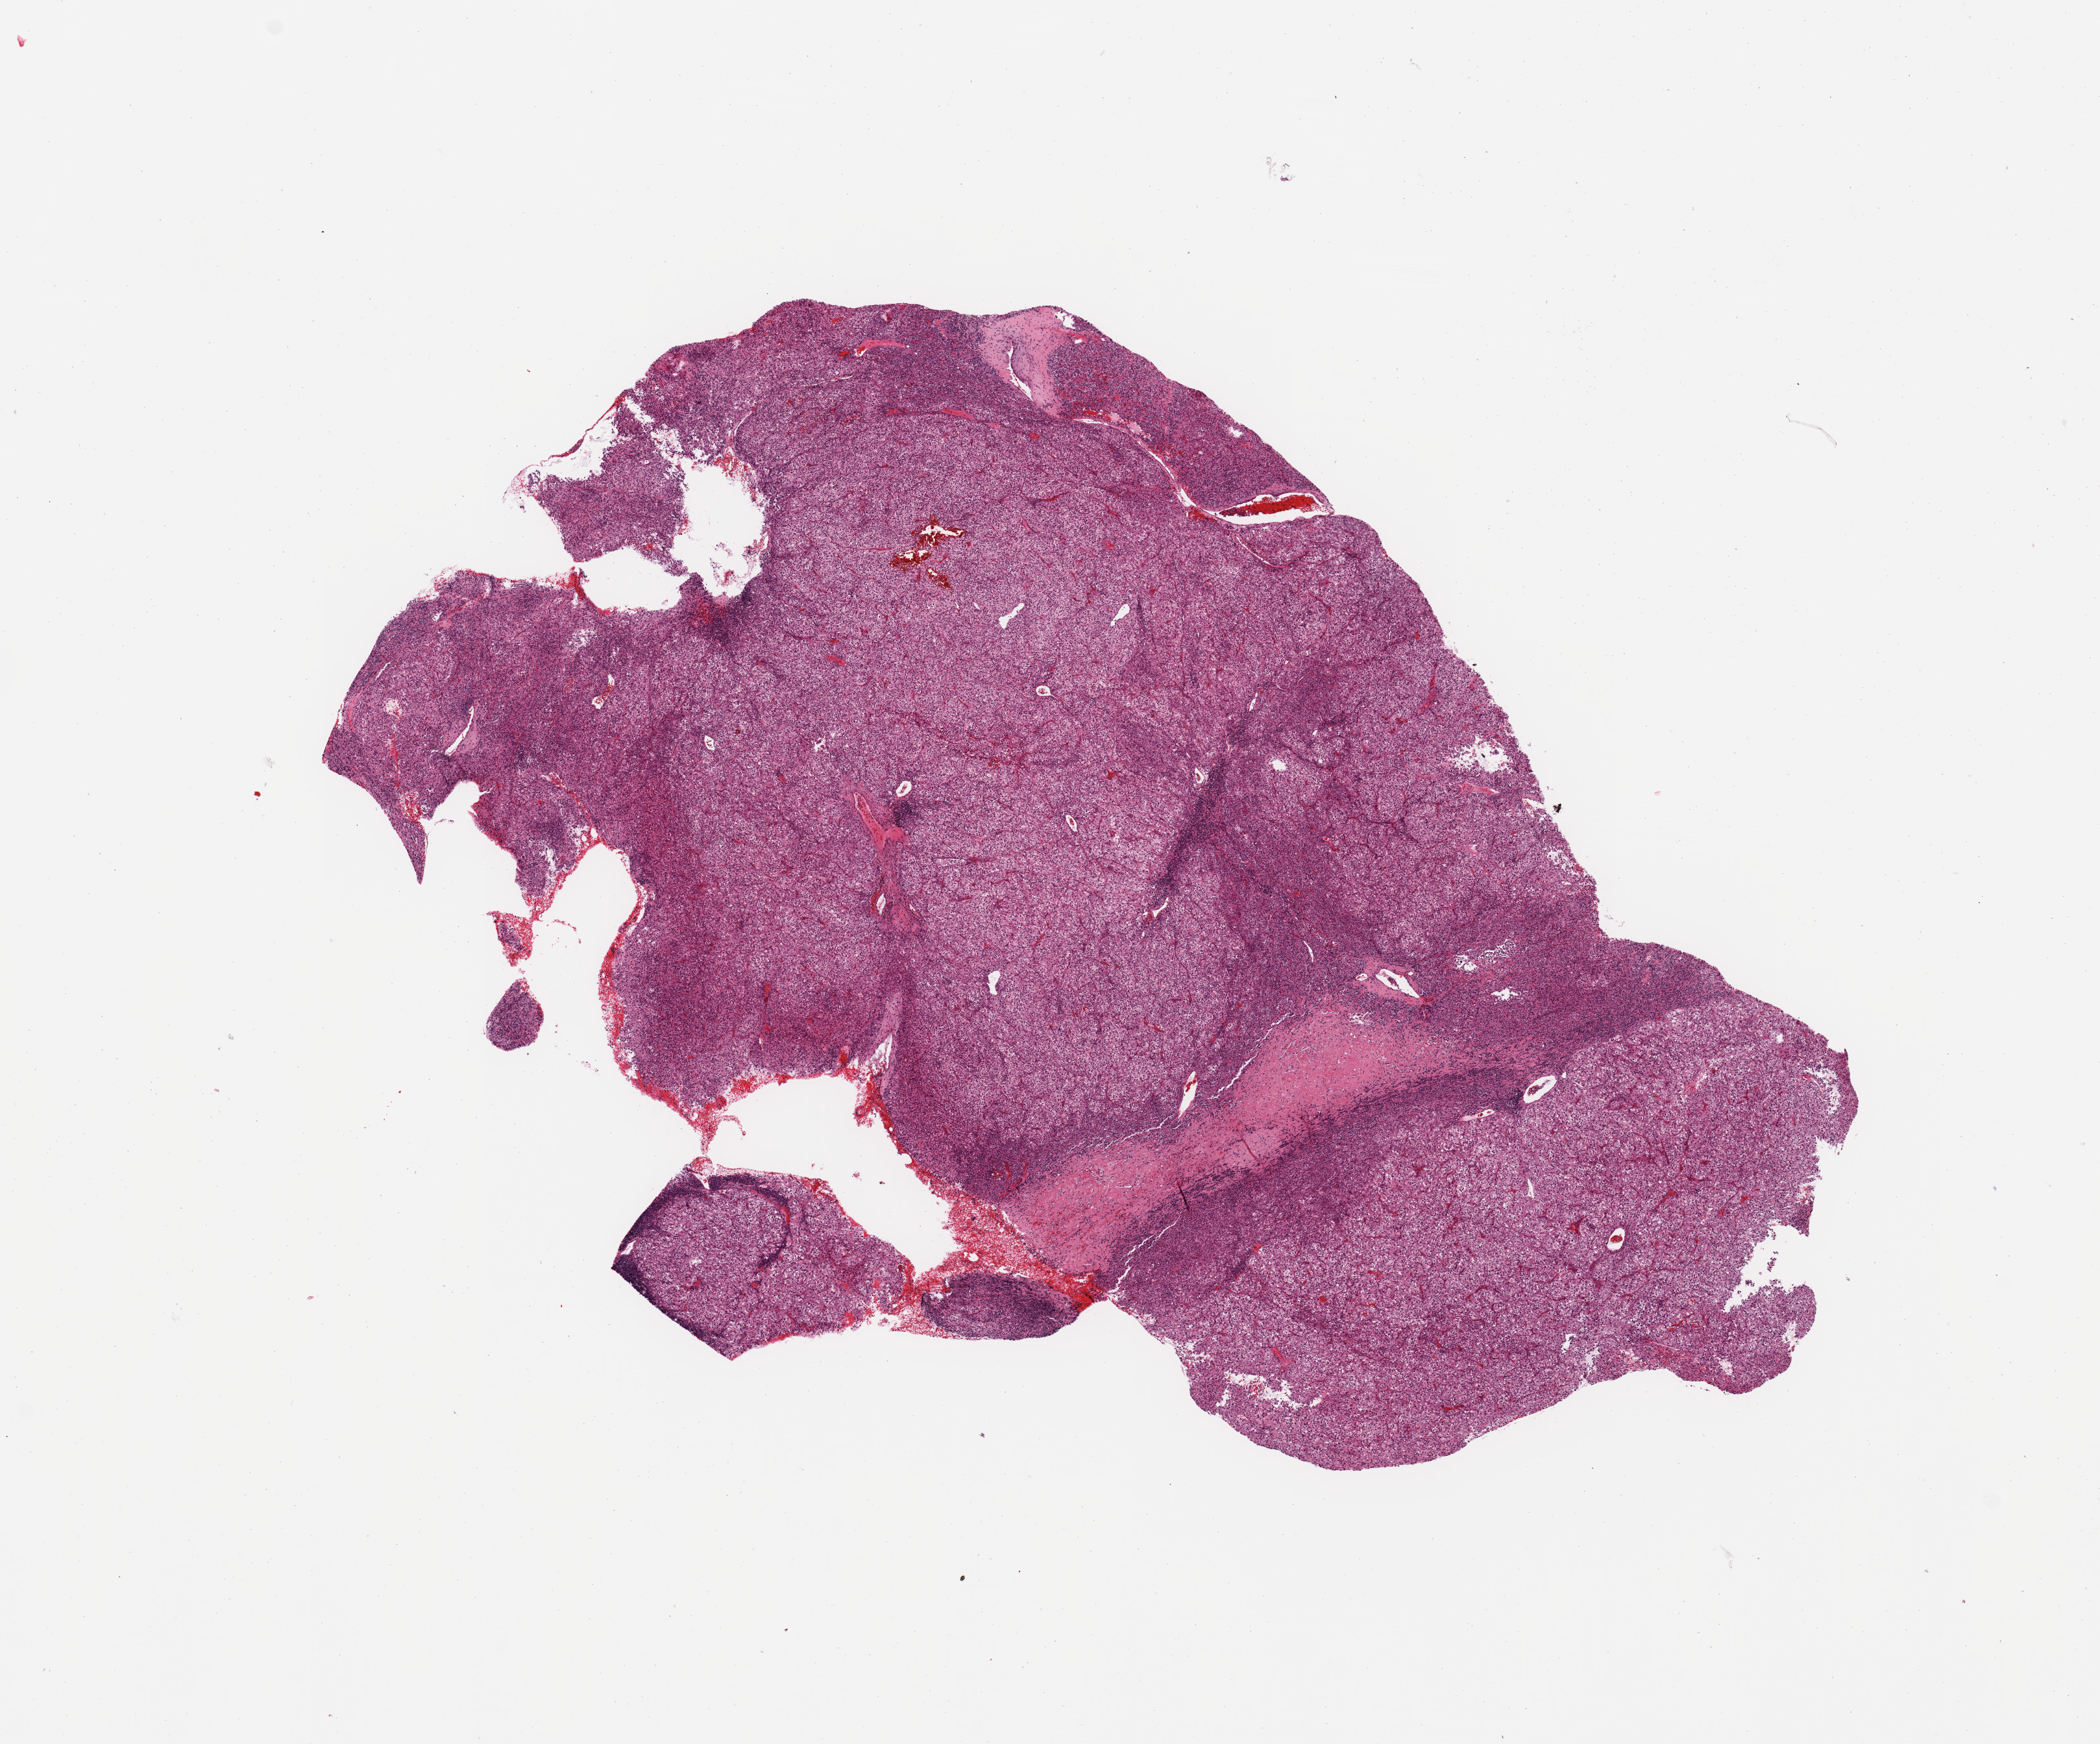
Digitized Hematoxylin and eosin (H&E) stained tissue section (whole slide) — a low-resolution overview of the entire scanned area, about 12.8 x 10.6 mm; tumour tissue sample, sampled site: kidney. Patient: male, age 52 years. Histologic grade: G4 (undifferentiated). Pathologist review of this section (percent, as recorded): tumour nuclei 85%, necrosis 5%.
AJCC pathologic stage: IV. Histologic diagnosis: Renal cell carcinoma, NOS.